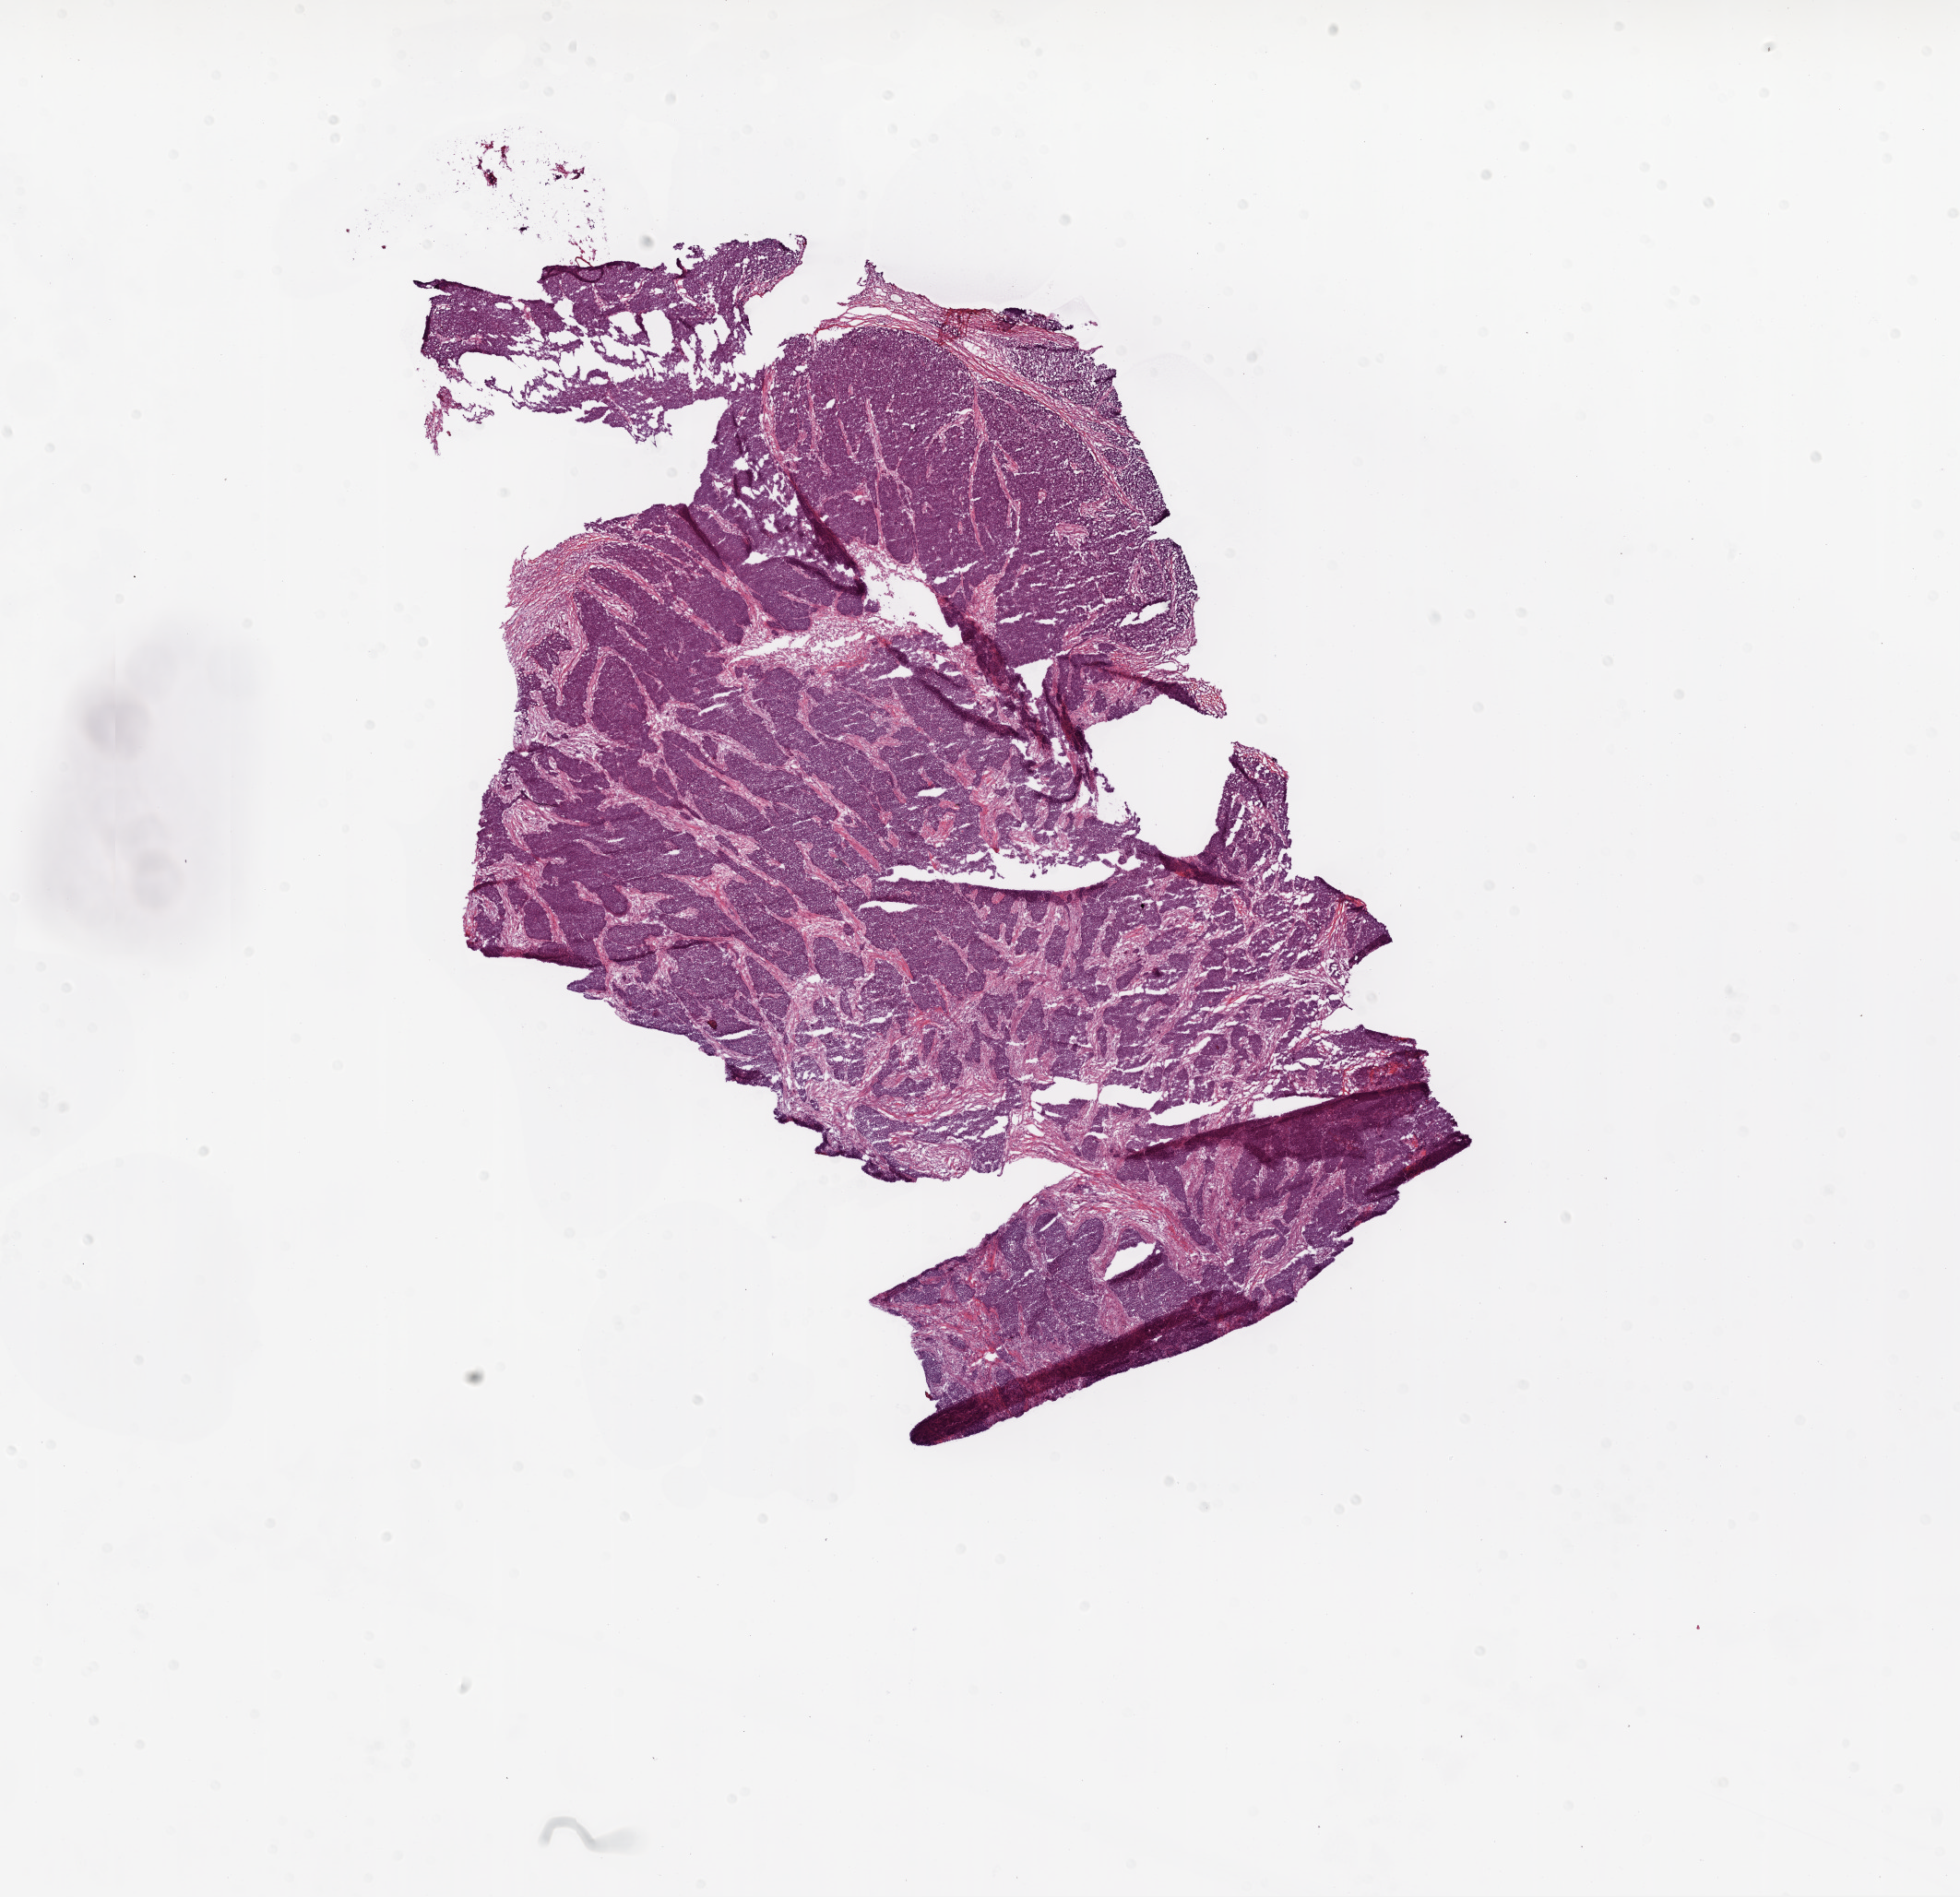
Digitized H&E-stained tissue section (whole slide) — low-resolution overview of the scanned area, about 17.1 x 16.5 mm (from a 20x scan), frozen section from the bottom of the tissue portion, primary tumour sample from the ovary. Female patient; age at initial diagnosis 45 years. Histologic grade: G3 (poorly differentiated). Pathologist review of this section (percent, as recorded): tumour cells 80%, tumour nuclei 80%, normal cells 0%, stromal cells 5%, necrosis 15%. Infiltration values recorded for this section: lymphocyte infiltration 0%, monocyte infiltration 0%, neutrophil infiltration 15%.
• laterality: bilateral
• pathologic diagnosis: Serous cystadenocarcinoma, NOS
• FIGO stage: IIIC